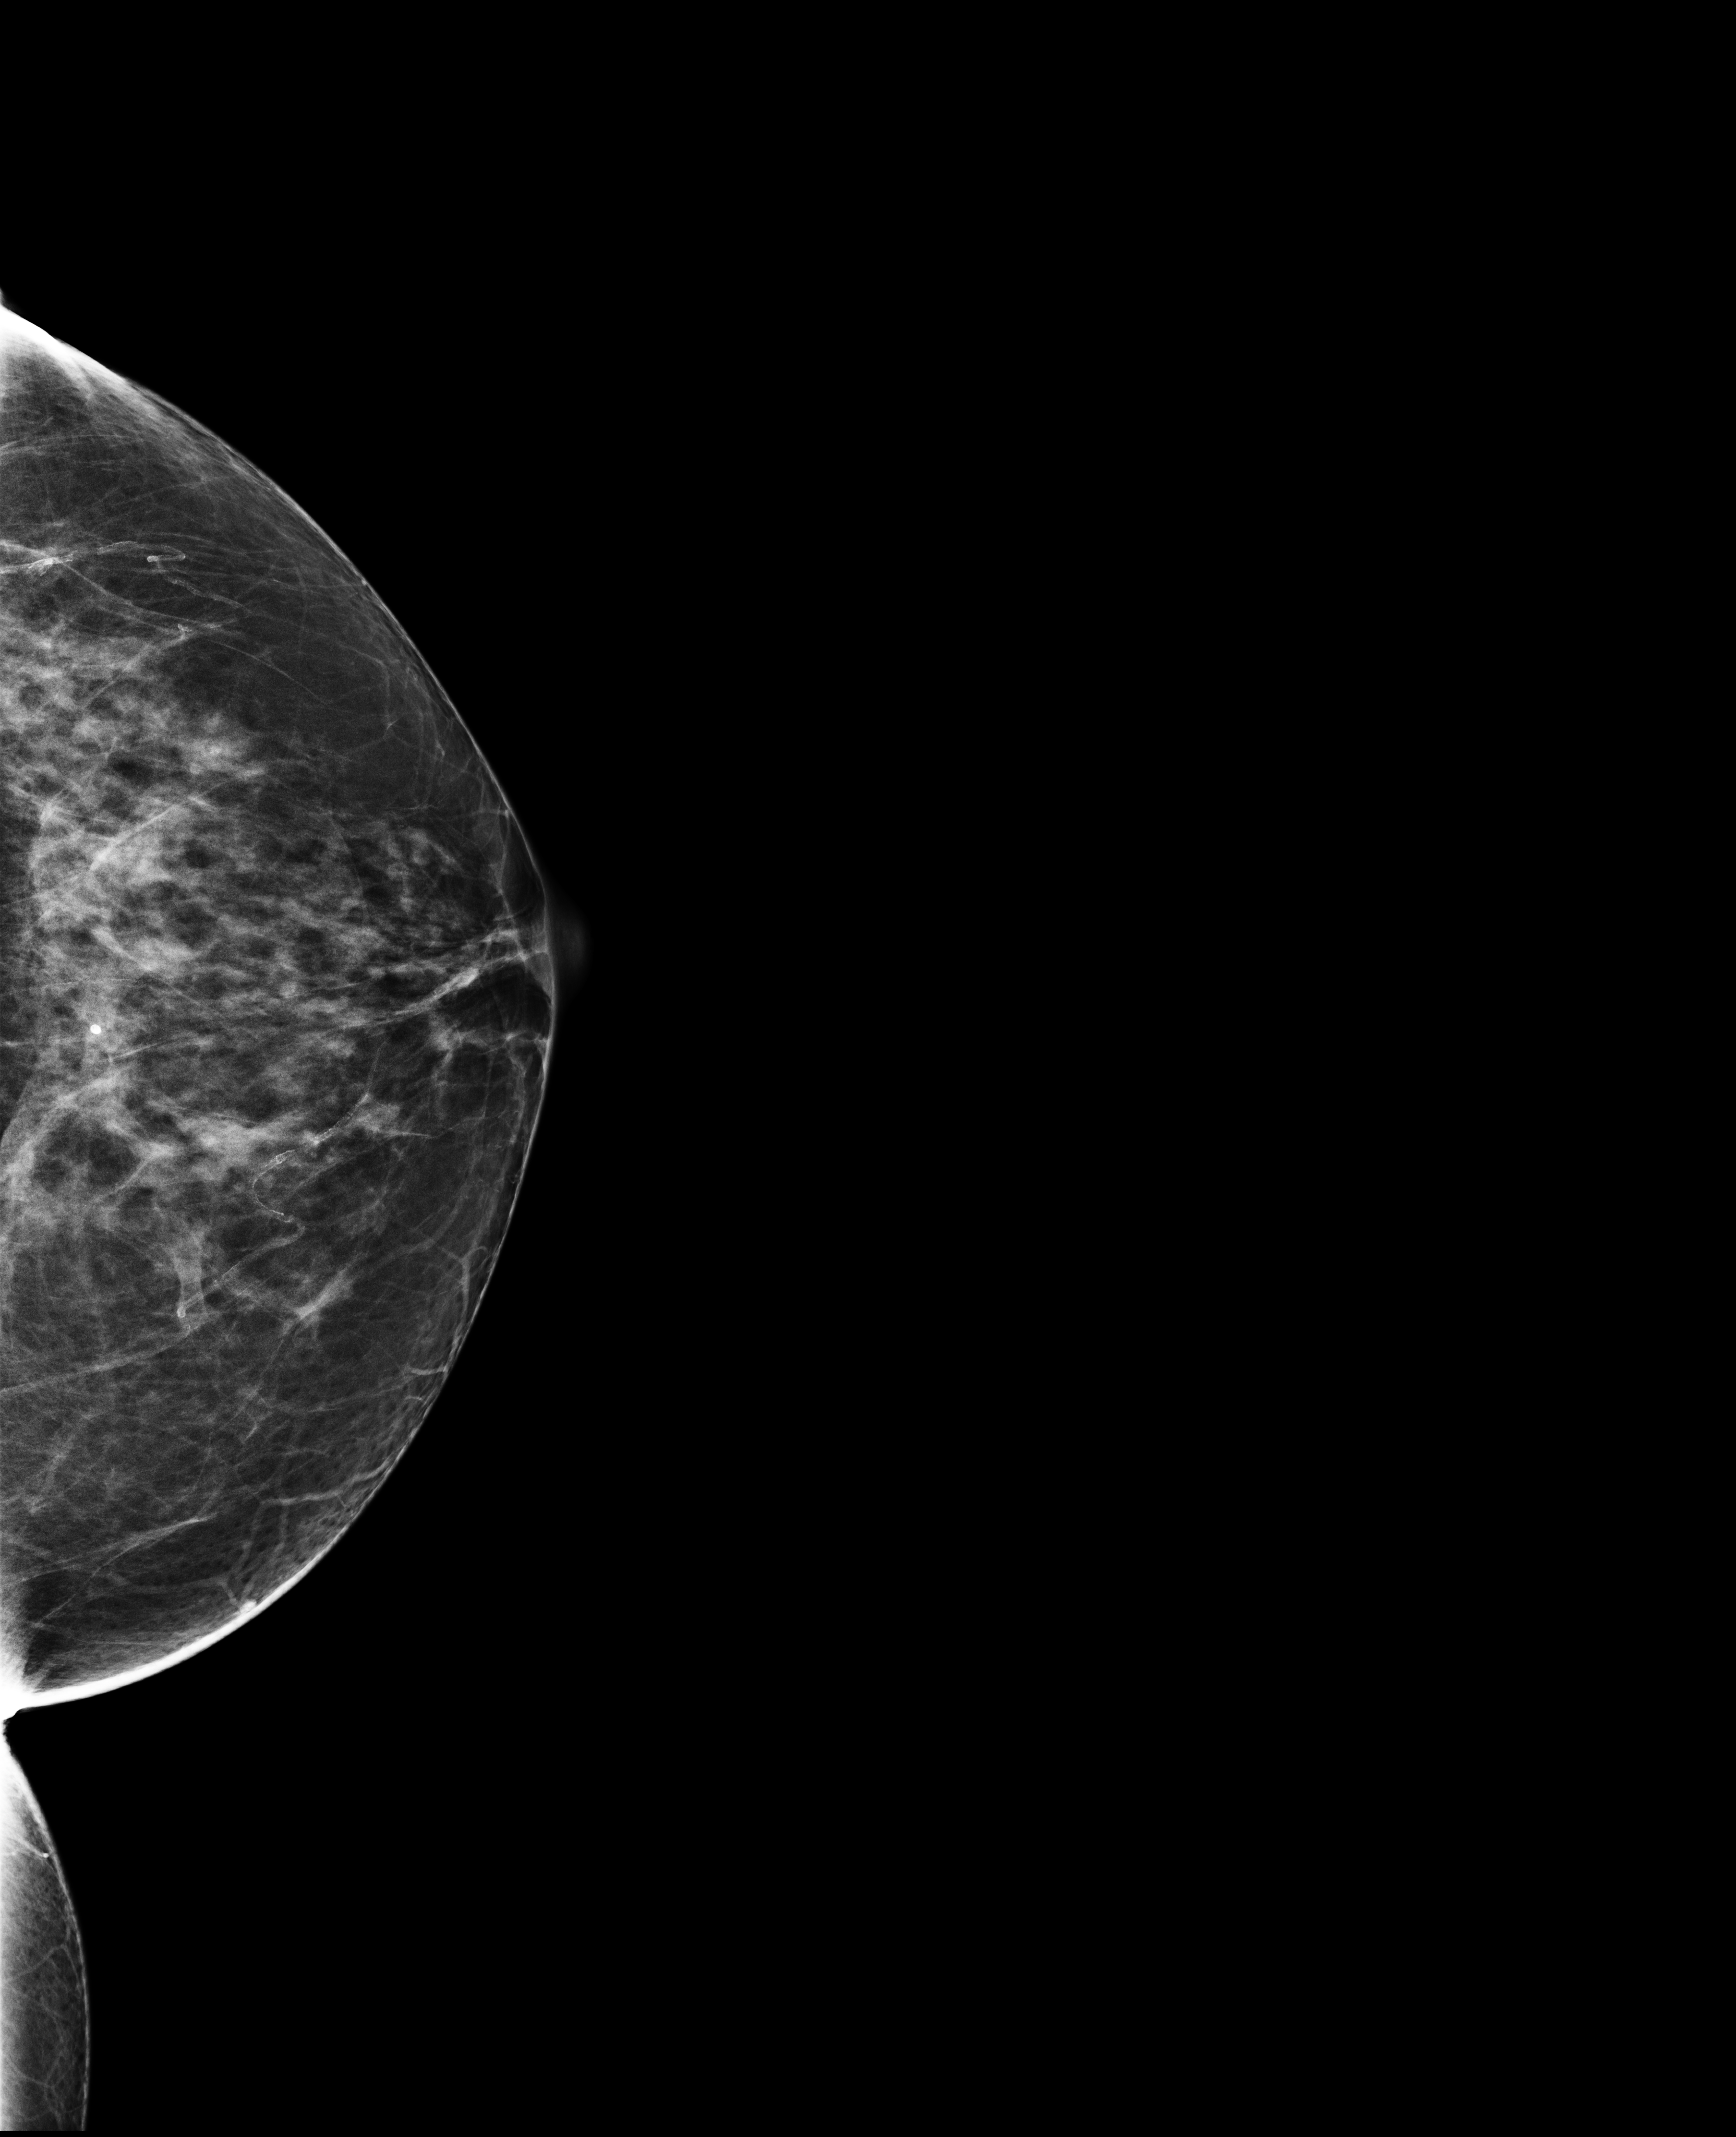
Full-field digital mammogram (FFDM), left breast, craniocaudal (CC) view, screening examination. Patient aged 67 years (female).
BI-RADS breast density category at the screening exam (both breasts, scale 1–4): 3. Final BI-RADS category for the screening round (tomosynthesis exam, both breasts): category 1. Recall: no recall after this screen.